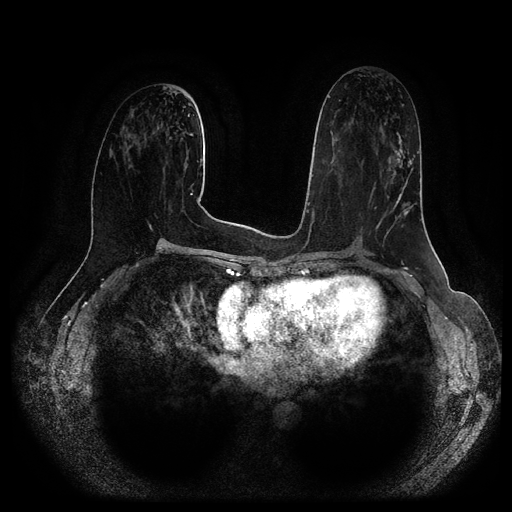
Breast MRI (dynamic contrast-enhanced, multi-phase), one axial slice; position 52 of 116 along the scan axis; dynamic contrast-enhanced series, time point 2 of 5 at this slice position (early post-contrast); 1.5 T; TE 2.6 ms, TR 5.2 ms; 2 mm slice thickness; 512 × 512 image matrix, field of view 380 × 380 mm. Female patient, age 57 years.
Outlined on this slice (semi-automatic segmentation, software-assisted and operator-edited):
- breast lesion (labelled 'tumour' in the annotation; benign lesions carry a separate 'benign' label): bounding box [x1, y1, x2, y2] px = [384, 134, 416, 227]